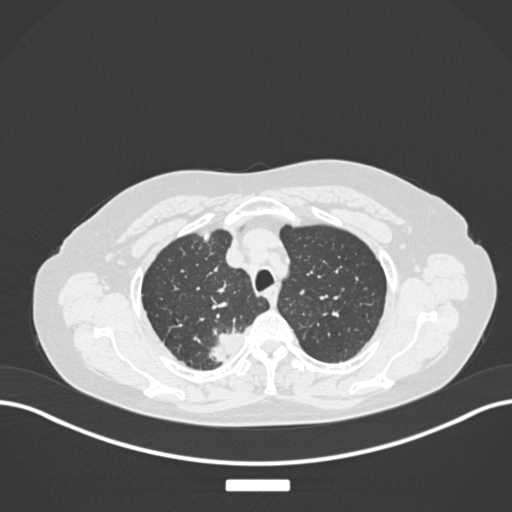
Chest CT, one axial slice; position 210 of 237 along the scan axis; reconstruction kernel B30f; lung window (W 1500 / L -600 HU); 1 mm slice thickness; 512 × 512 image matrix. Patient: female, 62 years. Case-level facts recorded for this patient, not image findings: clinical TNM (as recorded): T1c N1 M0.
Outlined on this slice (rectangle marked by the reading radiologist):
- lung tumour (recorded histology: squamous cell carcinoma): bounding box (x1, y1, x2, y2) in pixels: (203, 327, 256, 368)